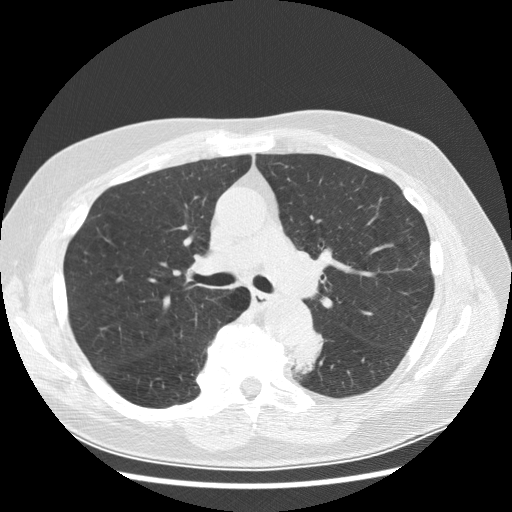
Low-dose screening chest CT, axial slice; first (baseline) screen; lung window (W 1500 / L -600 HU); 2.5 mm slice thickness; 120 kVp; slice 102 of 282 in the series. Male participant, aged 70 years at enrolment.
- Expert-annotated lung lesion, bounding box <278,331,328,381> (left, top, right, bottom; pixels).
- Screening reader's record for this exam (one nodule recorded; not confirmed to be the boxed lesion): non-calcified nodule or mass ≥4 mm, left lower lobe, 27 × 16 mm, spiculated (stellate) margins, soft tissue attenuation, pre-existing on the prior screen: yes; interval growth: yes.
- Lung cancer was diagnosed 97 days after this screen: papillary adenocarcinoma, NOS, left lower lobe, moderately differentiated (G2), stage IB (AJCC 6th edition), 35 mm at pathology.